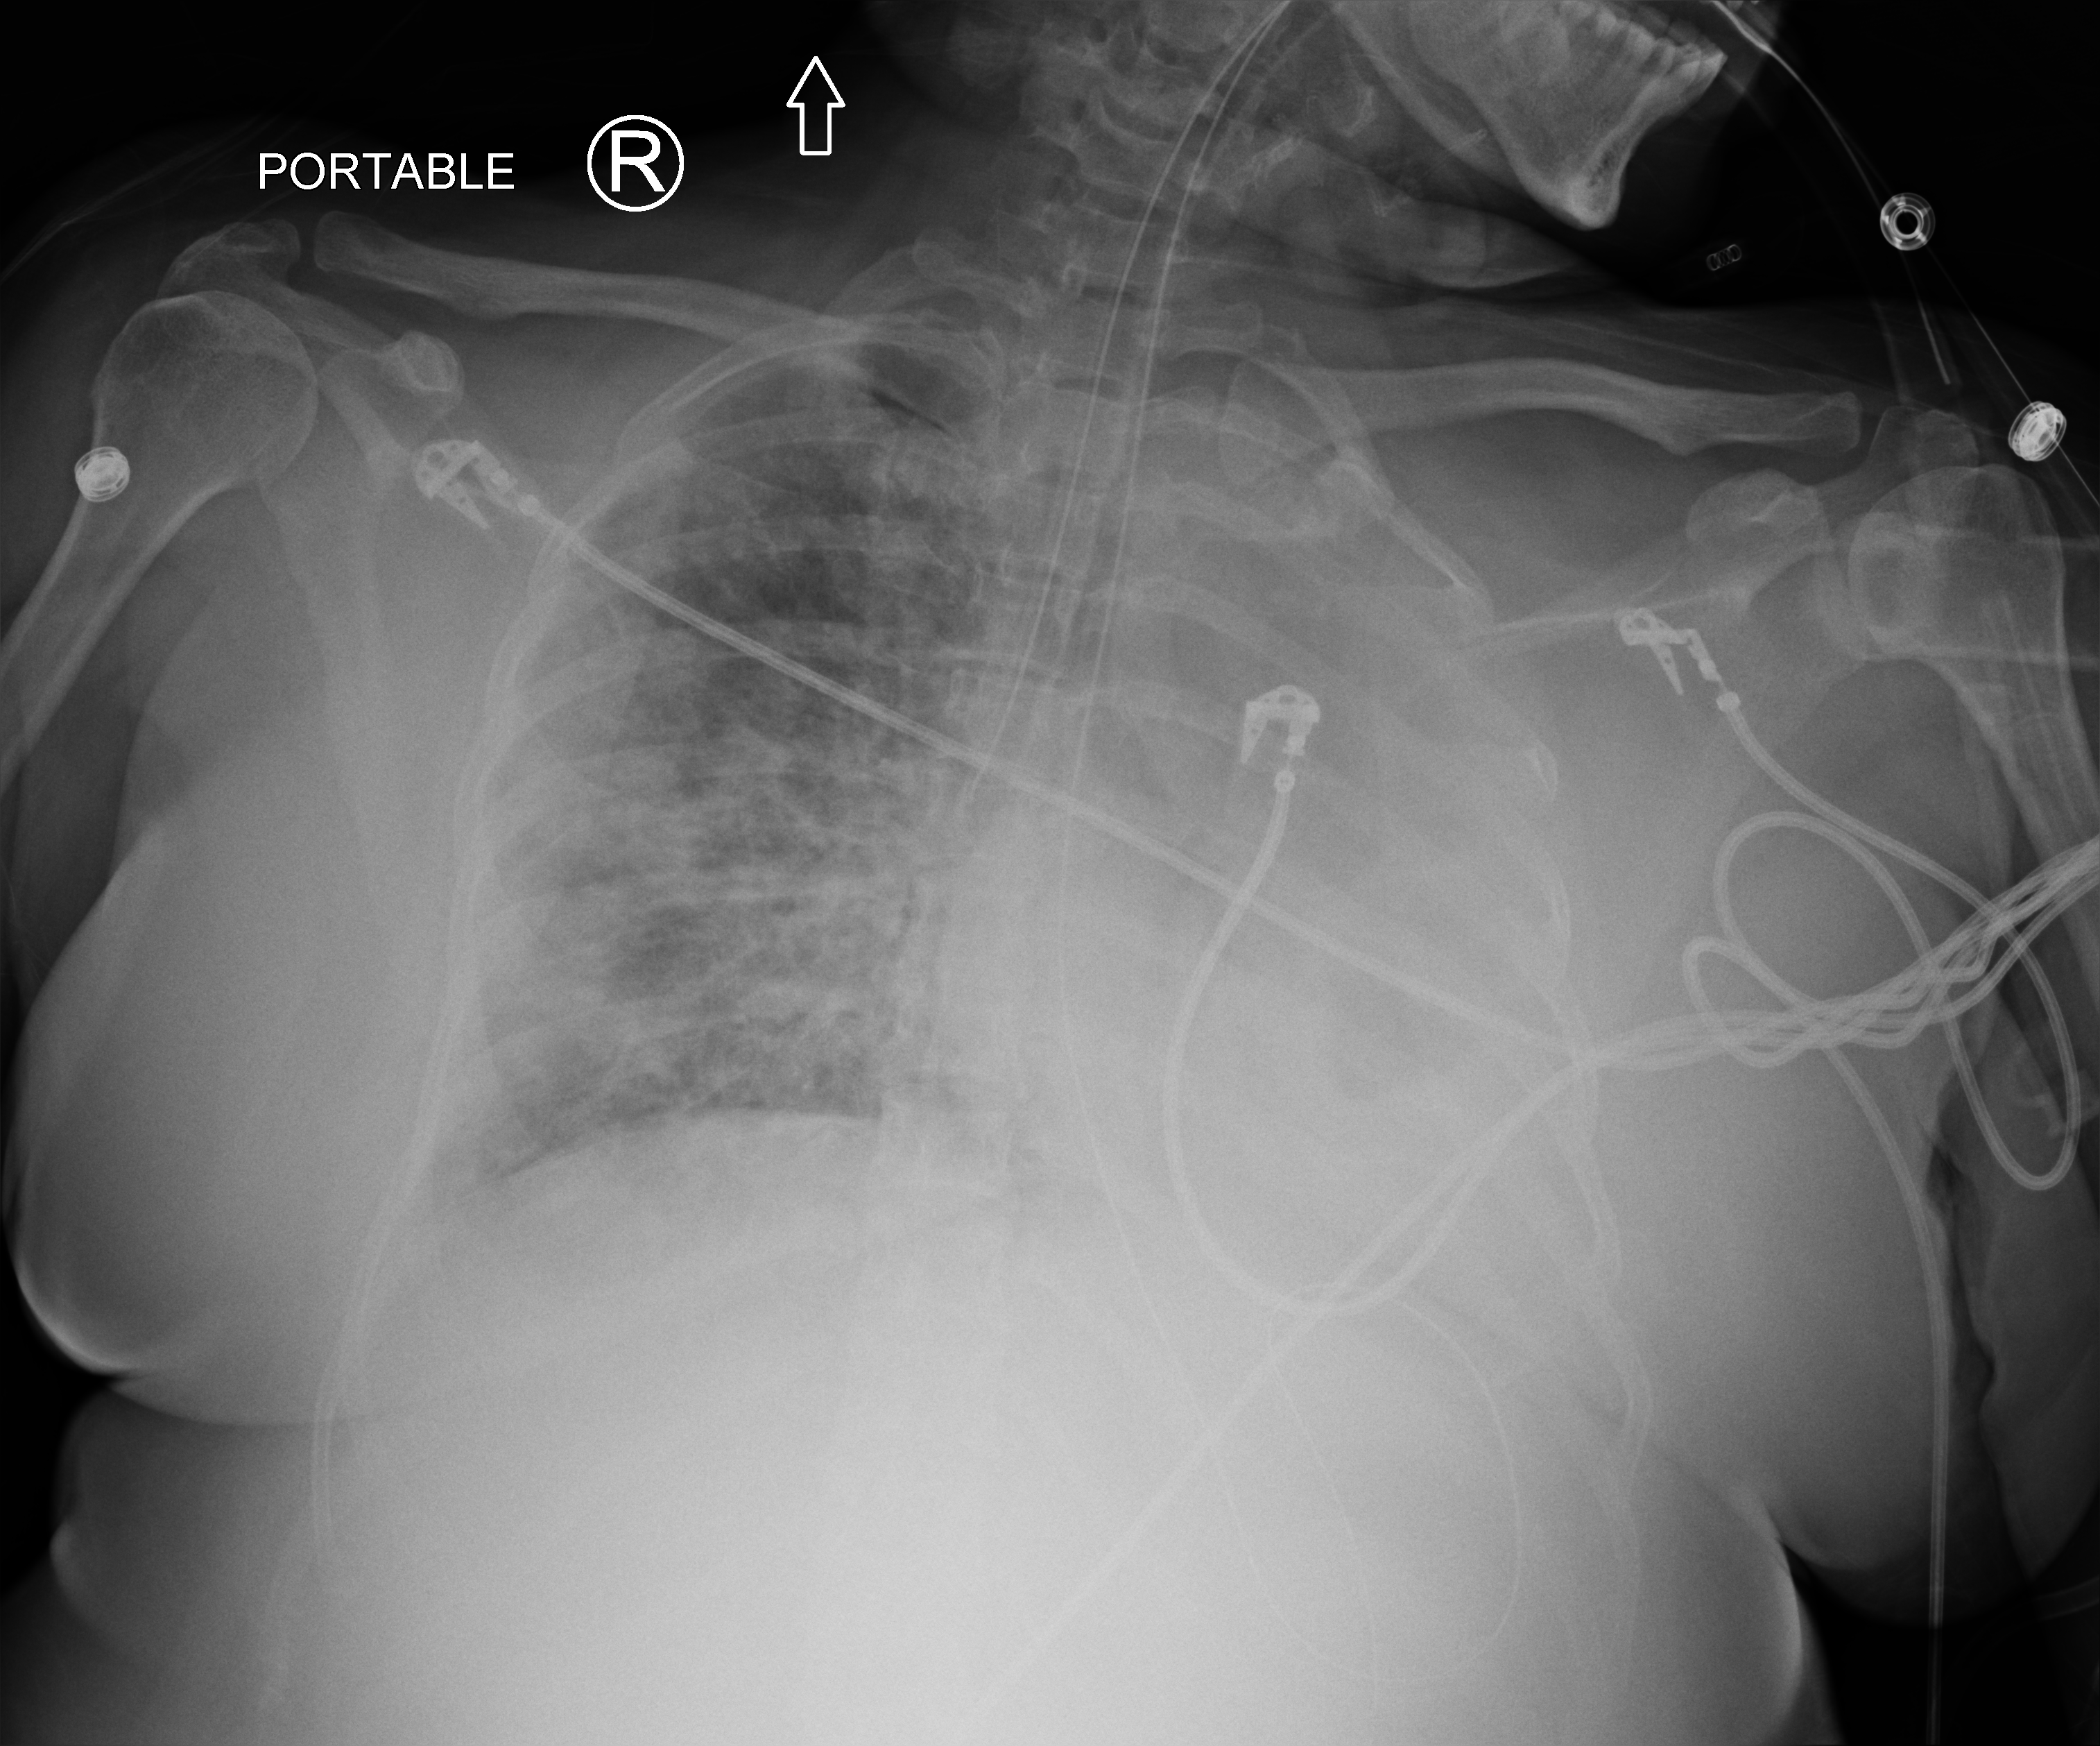
Portable chest radiograph, anteroposterior (AP) projection. Patient hospitalised with COVID-19, aged 18–59 years.
Admission-level facts for this patient (not findings on this image; timing relative to this image not recorded): smoking status (admission record): never.